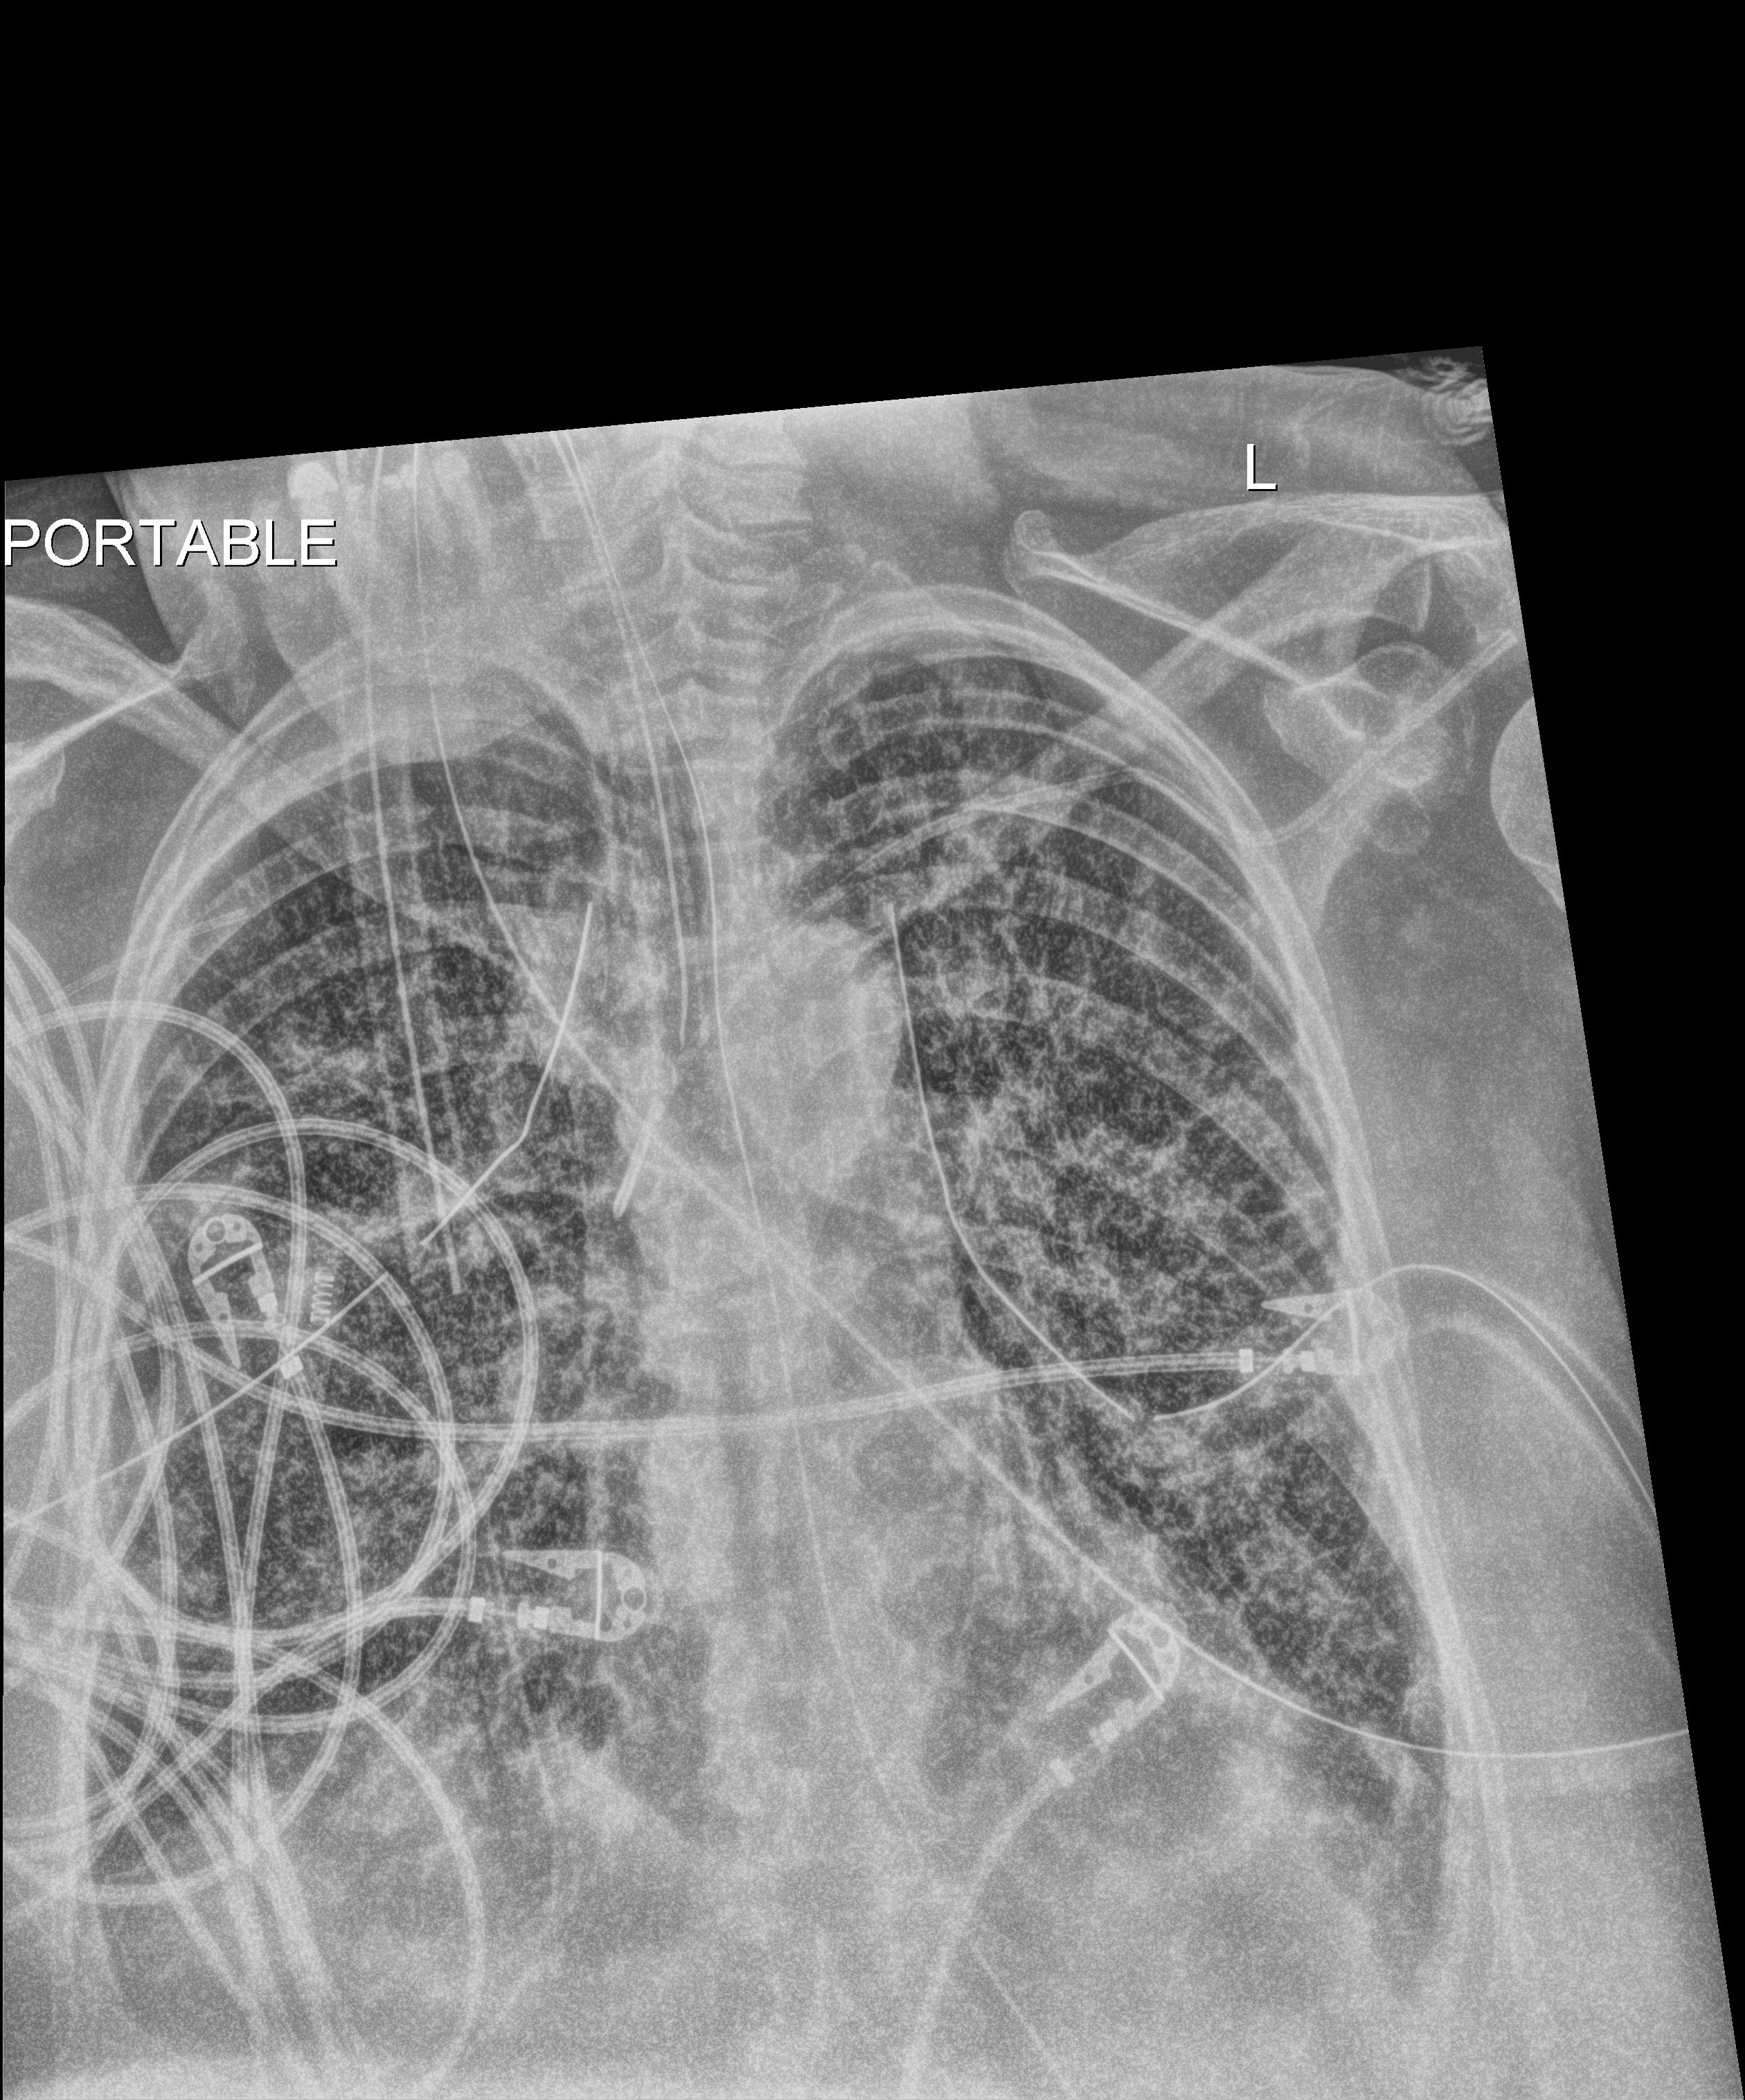
Portable chest radiograph; anteroposterior (AP) projection. Patient hospitalised with COVID-19; female, aged 60–74 years.
Hospital-stay facts (about this admission, not read from this image; timing relative to this image not recorded): hypertension (admission record): no.